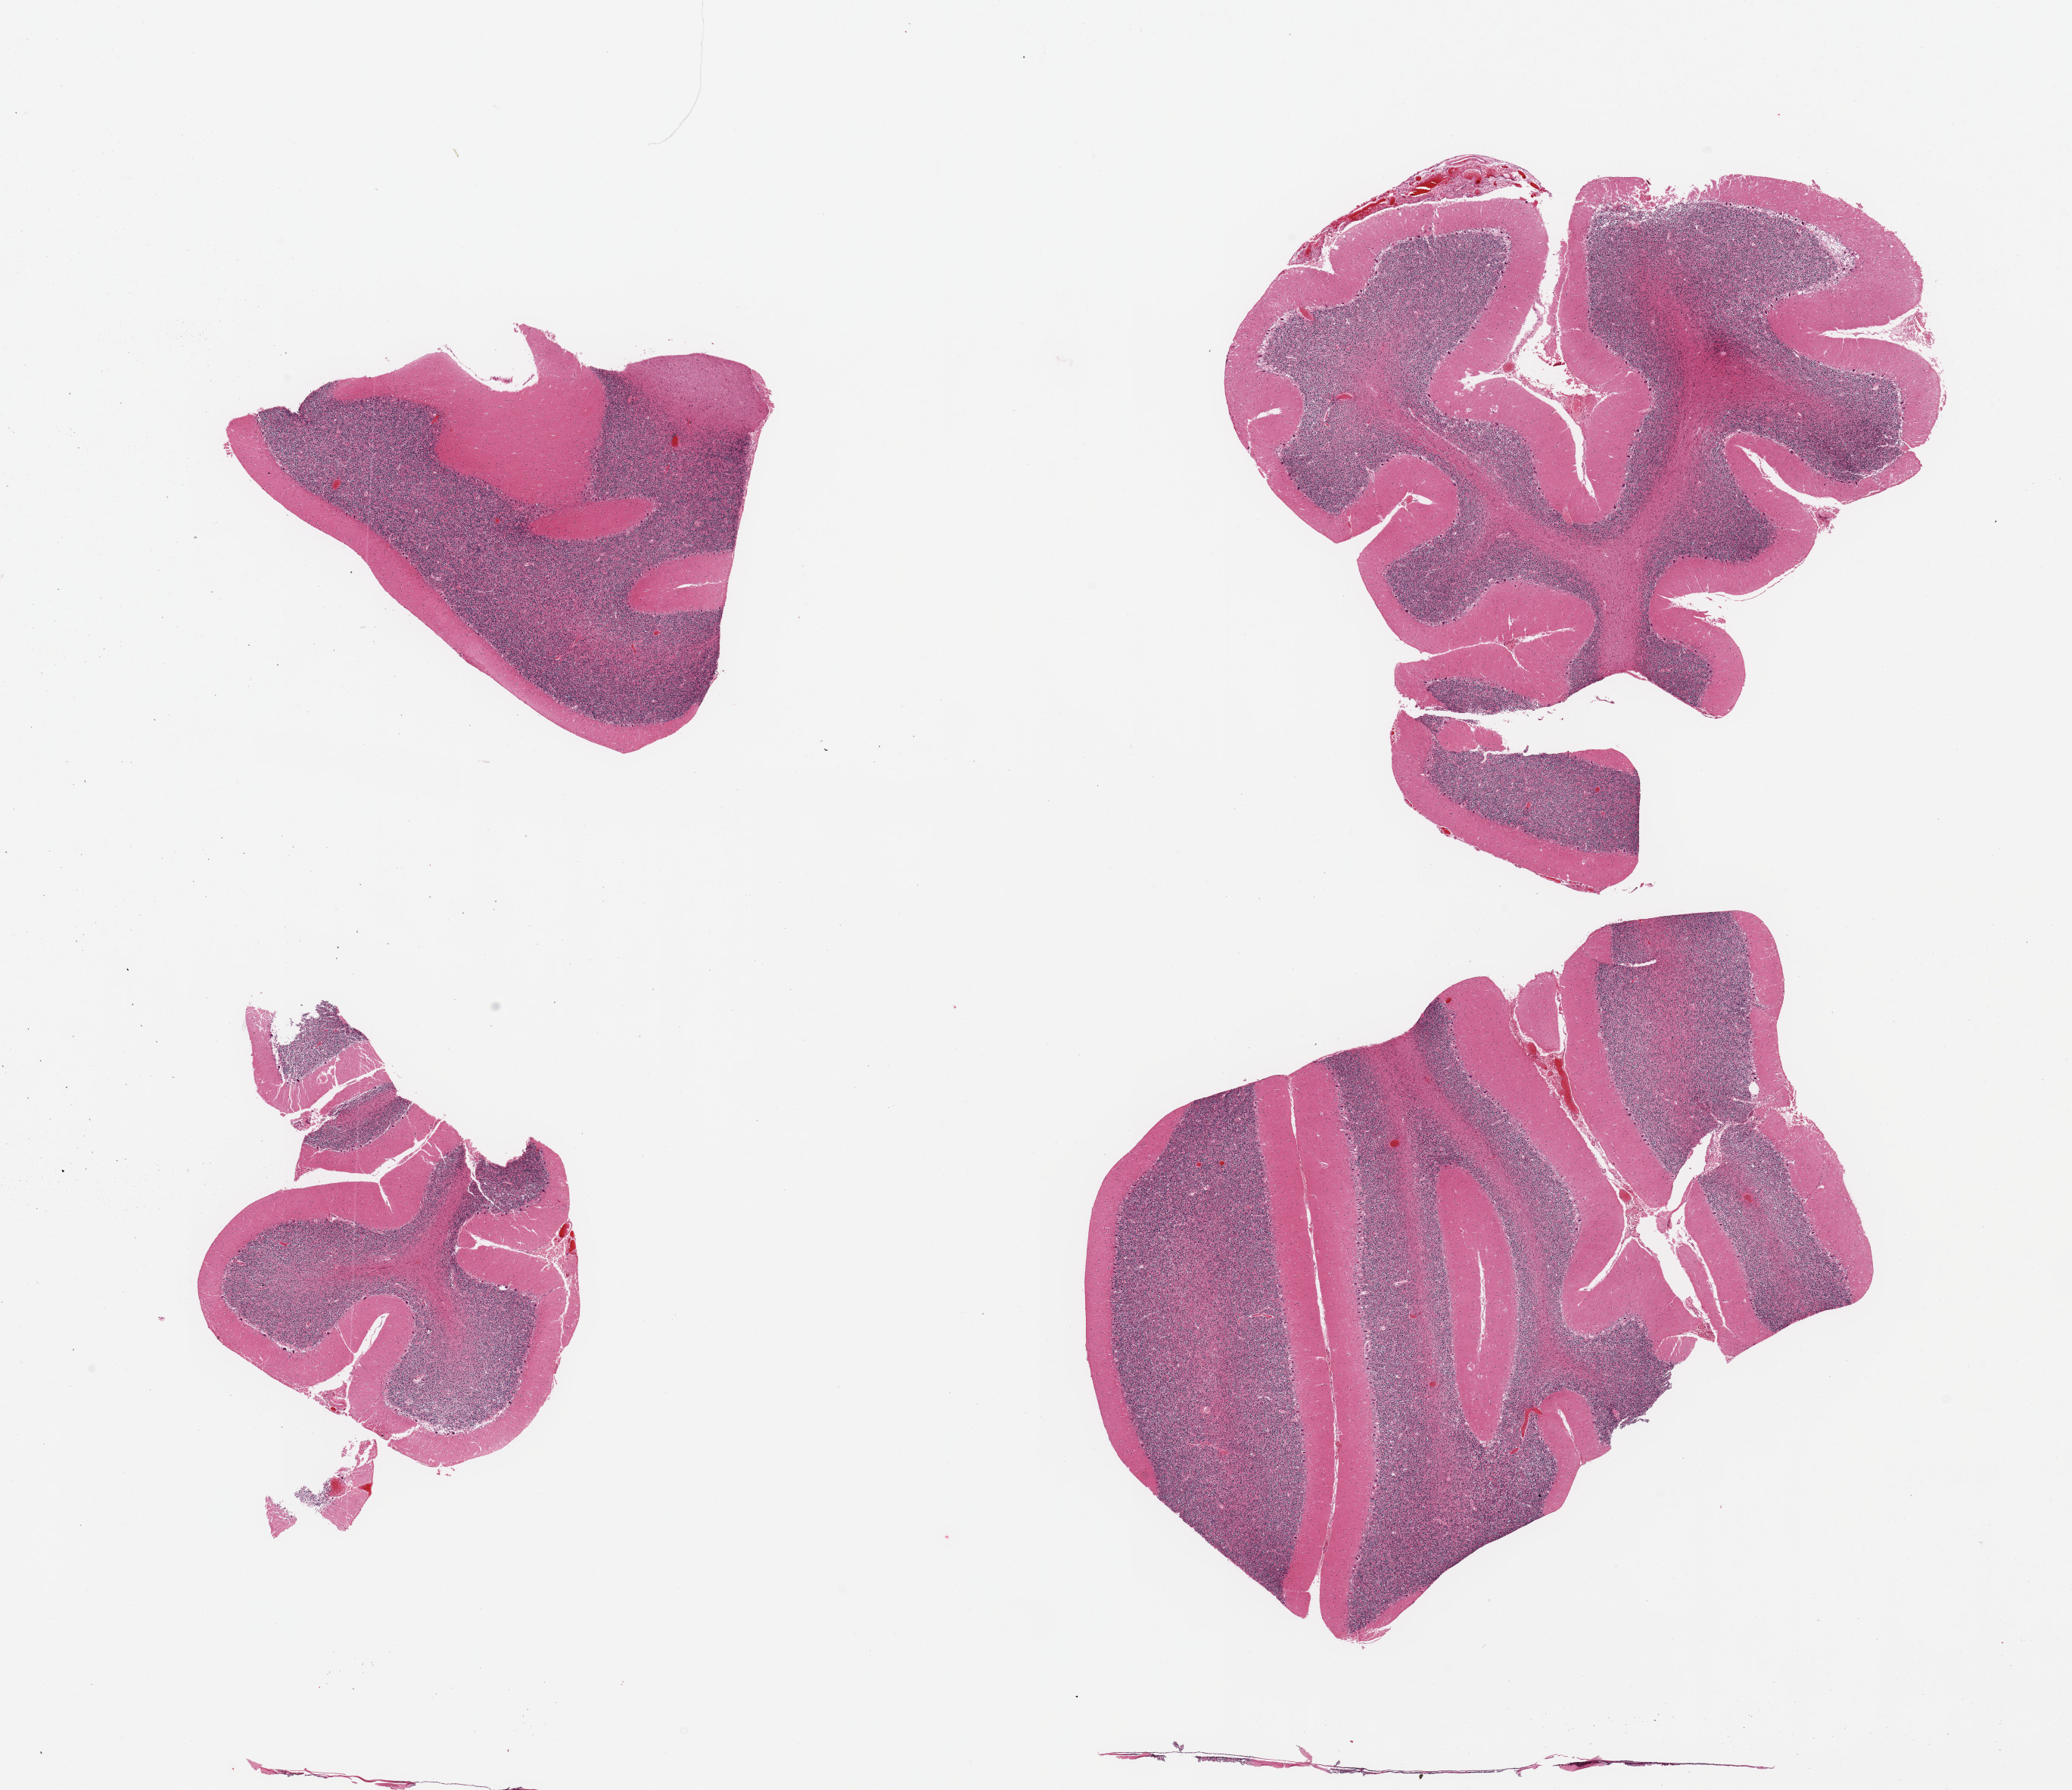
Whole-slide image, haematoxylin and eosin stain, a low-resolution overview of the entire scanned area, about 21.7 x 18.7 mm, PAXgene-fixed, paraffin-embedded tissue, sampled site (target tissue): cerebellum, tissue donor sample. Male donor.
Review note (as recorded): 4 pieces; small portion of residual attached meninges.